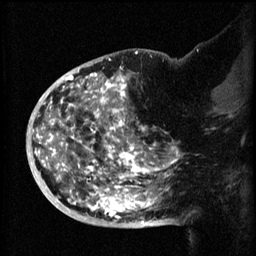
Breast MRI (dynamic contrast-enhanced), one sagittal slice; slice 35 of 60 in the series (ordered by position); 3 images stored at this slice position (order not interpretable as contrast timing); 1.5 T; TE 4.2 ms, TR 8.2 ms; 2 mm slice thickness; 256 × 256 image matrix, field of view 200 × 200 mm. Patient: female, 50 years.
Annotated regions visible in this slice (semi-automatic segmentation, software-assisted and operator-edited):
- analysis volume of interest (the breast-tissue region the enhancement analysis was run in; not a lesion): bounding box (x1, y1, x2, y2) in pixels: (44, 72, 173, 219)
- tumour enhancement mask (voxels above the 70 % enhancement threshold inside the analysis volume of interest): (44, 72, 173, 219)